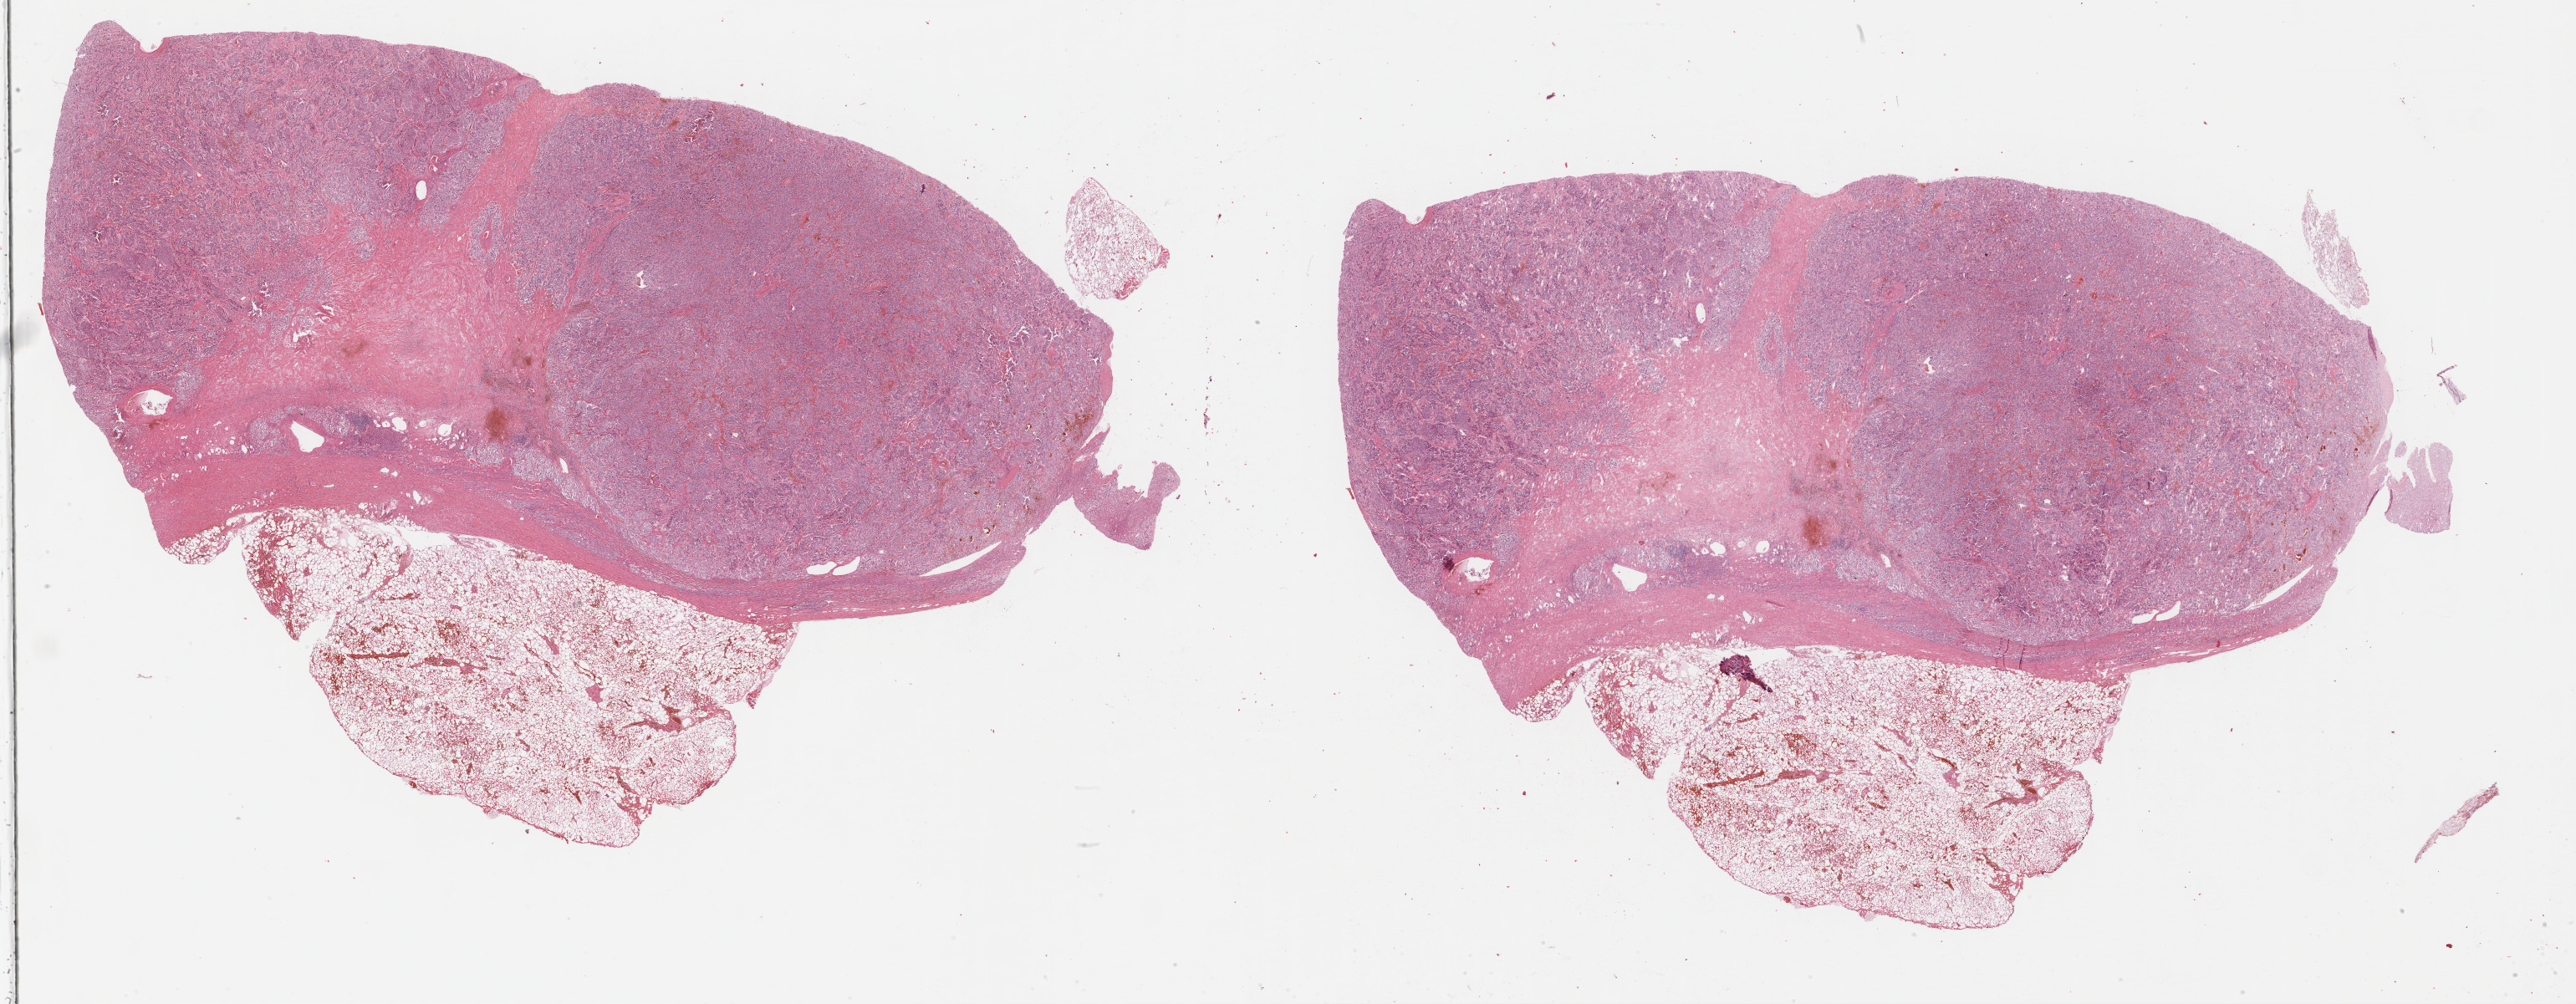
Whole-slide histology image, H&E-stained, shown as a low-resolution overview of the whole scanned area (about 49.8 x 19.4 mm, from a 40x scan), formalin-fixed paraffin-embedded (FFPE) diagnostic section, sample: primary tumour, adrenal gland. Male patient; age at initial diagnosis 34 years.
* laterality: left
* pathologic diagnosis: Pheochromocytoma, NOS